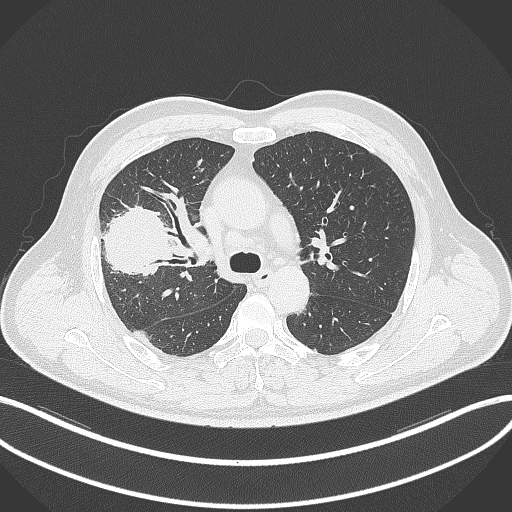
Chest CT, one axial slice; slice 221 of 348 in the series (ordered by position); reconstruction kernel B70f; 120 kVp; lung window (W 1500 / L -600 HU); 1 mm slice thickness; 512 × 512 image matrix, field of view 400 × 400 mm. Male patient, age 55 years. From the clinical record (not read from this slice): clinical TNM (as recorded): T3 N2 M1.
Annotated regions visible in this slice (bounding box drawn by a radiologist):
- lung tumour (recorded histology: adenocarcinoma): bounding box <98,202,169,281> (left, top, right, bottom; pixels)